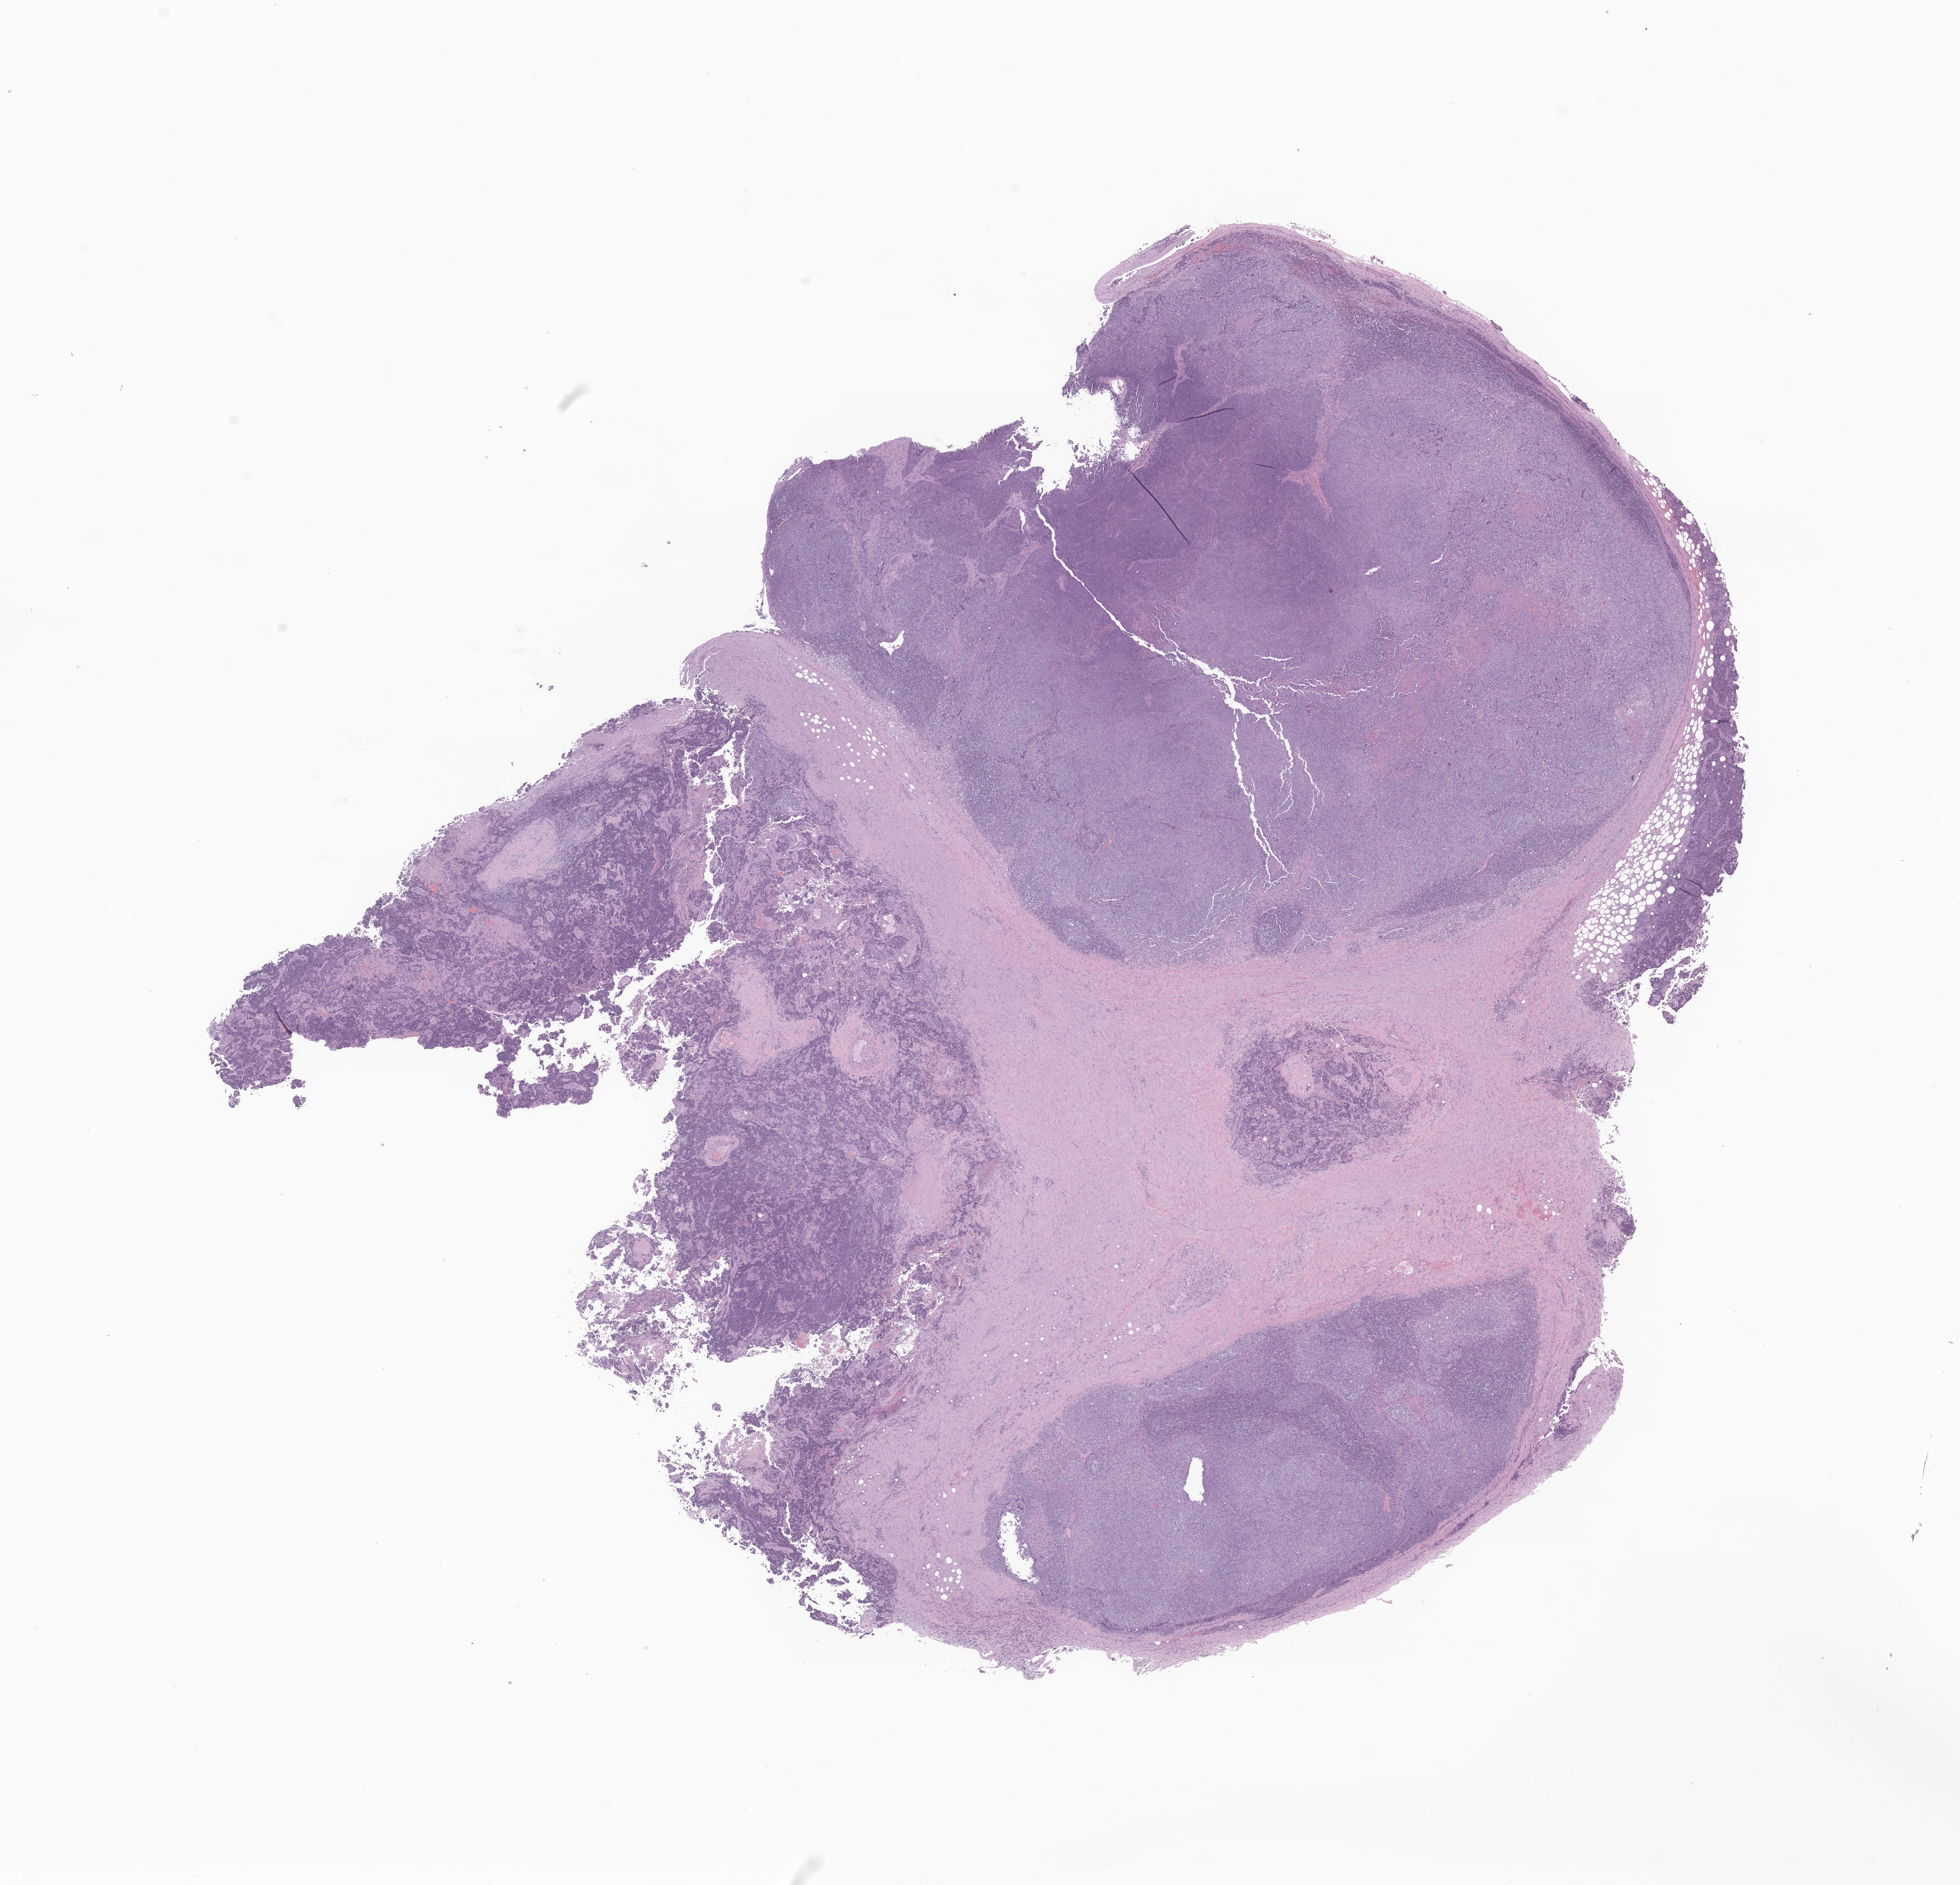
H&E whole-slide image of tumor tissue from the vagina — a low-resolution overview of the entire scanned area, about 18.2 x 17.5 mm, FFPE section. Female patient, age 139 months.
- recorded diagnosis: Rhabdomyosarcoma, NOS